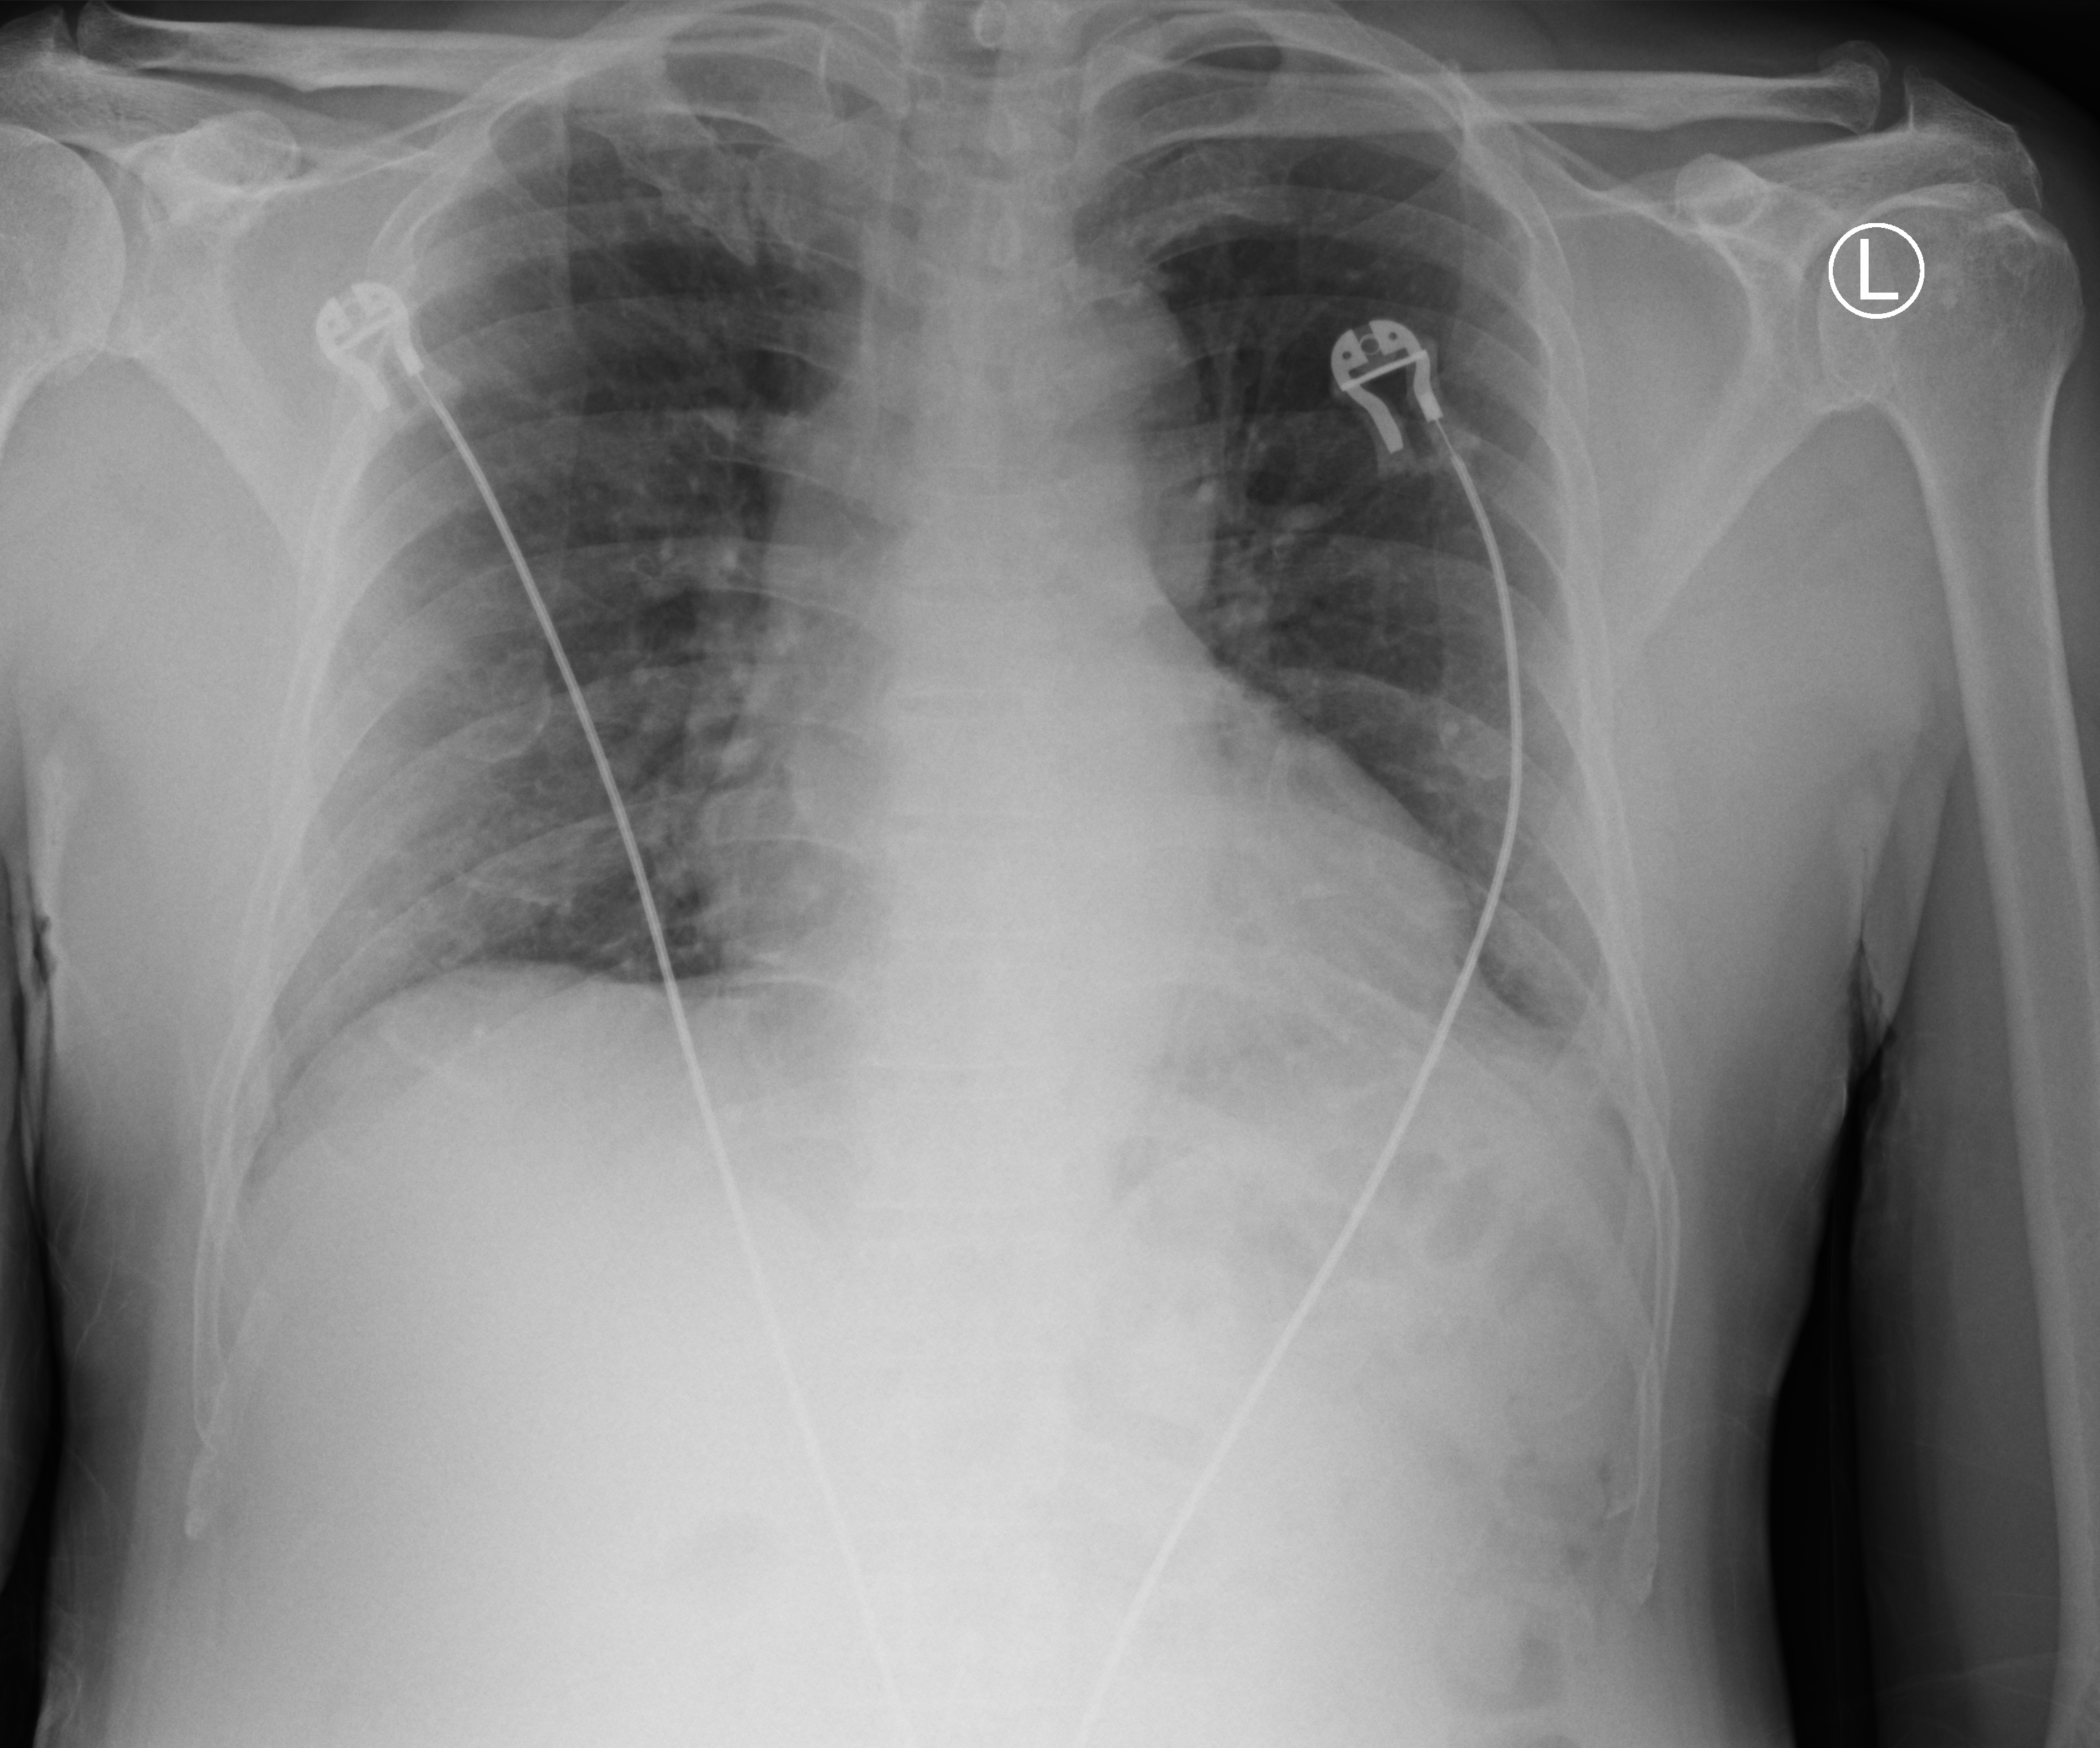
Portable chest radiograph, anteroposterior (AP) projection. Patient hospitalised with COVID-19; male, aged 60–74 years.
From the hospital-stay record, not from the radiograph (when in the stay this image was taken is not recorded): COPD (admission record): no.